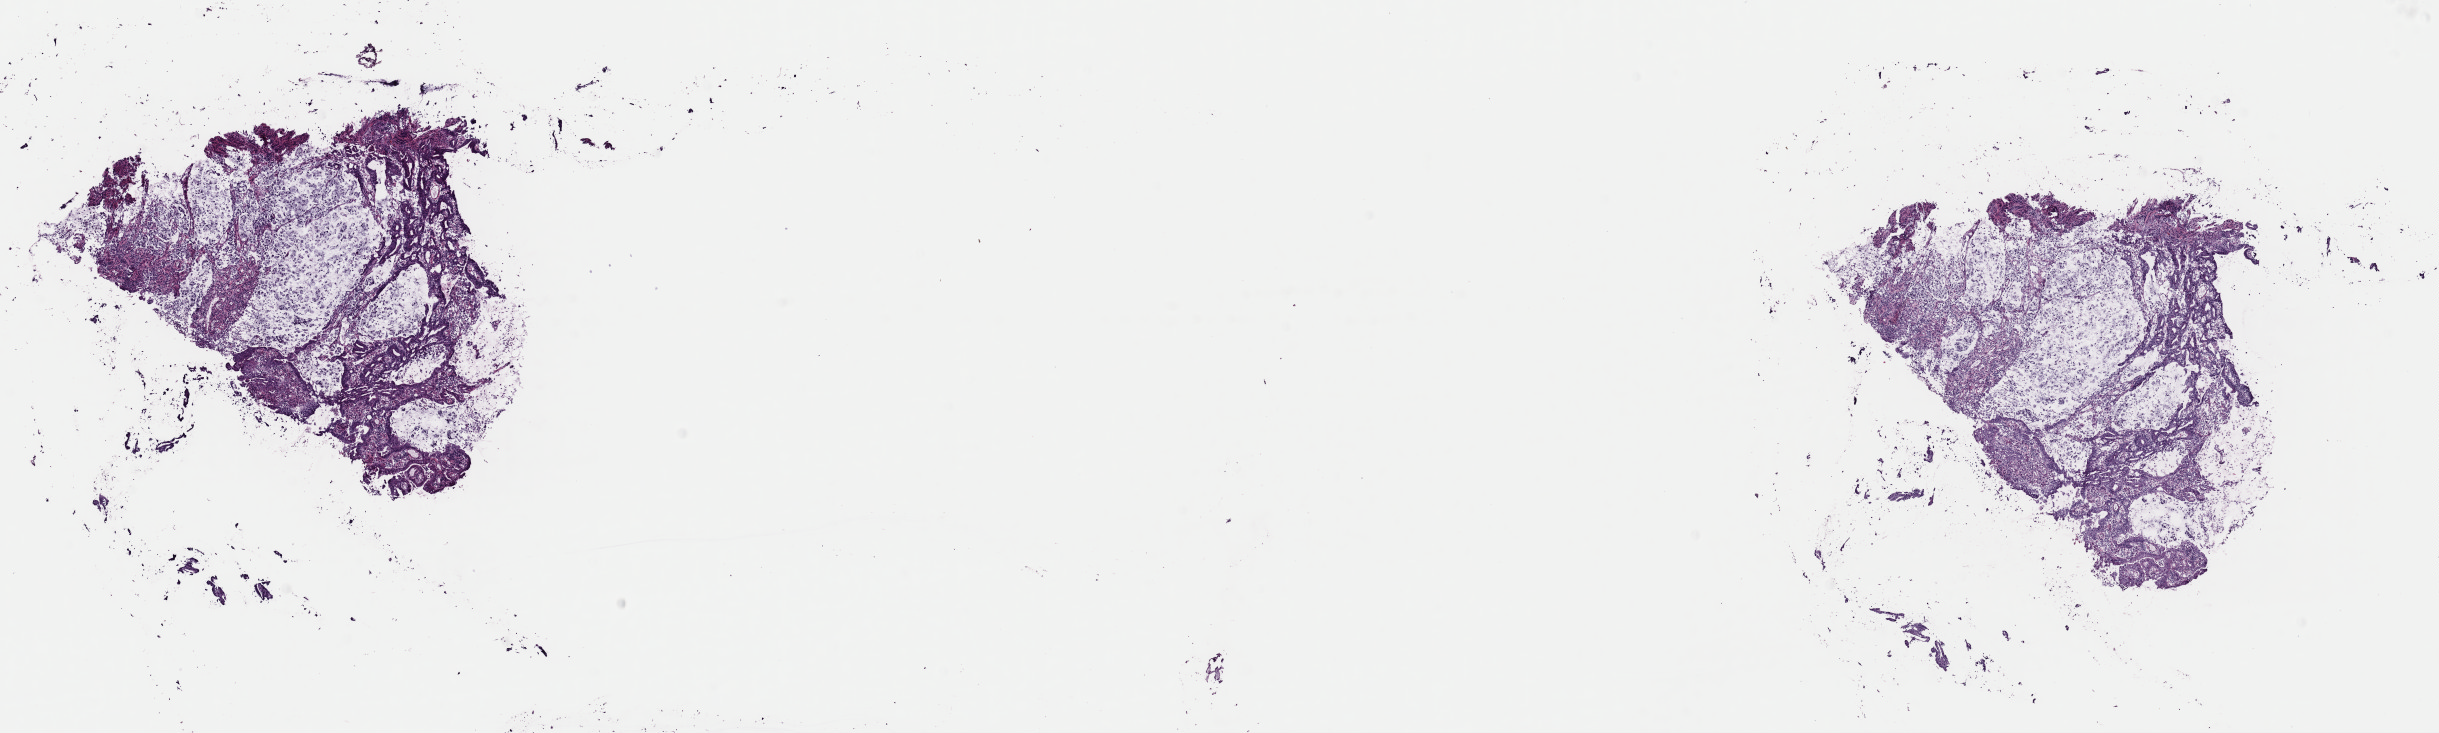
Digitized H&E tissue section (whole slide), low-resolution overview of the scanned area, about 19.3 x 5.8 mm (acquisition: 40x scan); frozen section; primary tumour sample from the stomach. Male, age 70 years at initial diagnosis. Histologic grade: G3 (poorly differentiated). Composition of this section per pathologist review: tumour cells 100%, tumour nuclei 70%, normal cells 0%, stromal cells 0%, necrosis 0%. Infiltration values recorded for this section: lymphocyte infiltration 2%, monocyte infiltration 5%, neutrophil infiltration 0%.
AJCC pathologic stage: IIIB (7th edition). Histologic diagnosis: Mucinous adenocarcinoma (gastric antrum).